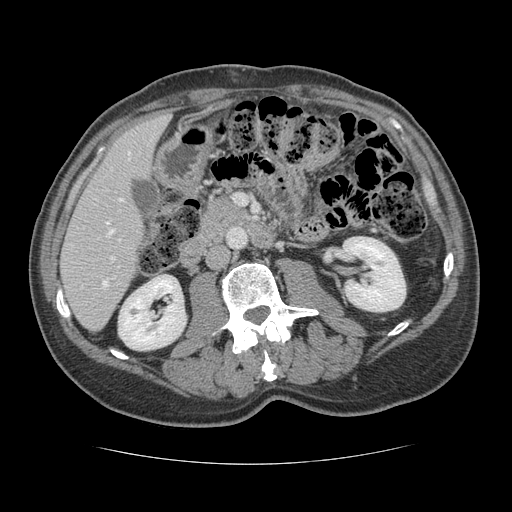
Contrast-enhanced abdominal CT, one axial slice. Slice 52 of 134 in the series (ordered by position). Reconstruction kernel STANDARD. Intravenous contrast given. Soft-tissue window (W 400 / L 40 HU). 2.5 mm slice thickness. 512 × 512 image matrix, field of view 377 × 377 mm. Male patient, age 68 years. Case-level facts recorded for this patient, not image findings: diagnosis: colorectal cancer liver metastases, imaged before liver resection; multiple liver metastases: yes; largest metastasis: 2.2 cm; chemotherapy before resection: no.
Outlined on this slice (manually delineated by an expert):
- hepatic veins: bounding box (x1, y1, x2, y2) in pixels: (106, 152, 130, 234)
- liver: (62, 115, 168, 330)
- planned liver remnant (the part of the liver to remain after resection): (62, 116, 168, 330)
- portal vein (with intrahepatic branches): (102, 257, 114, 286)